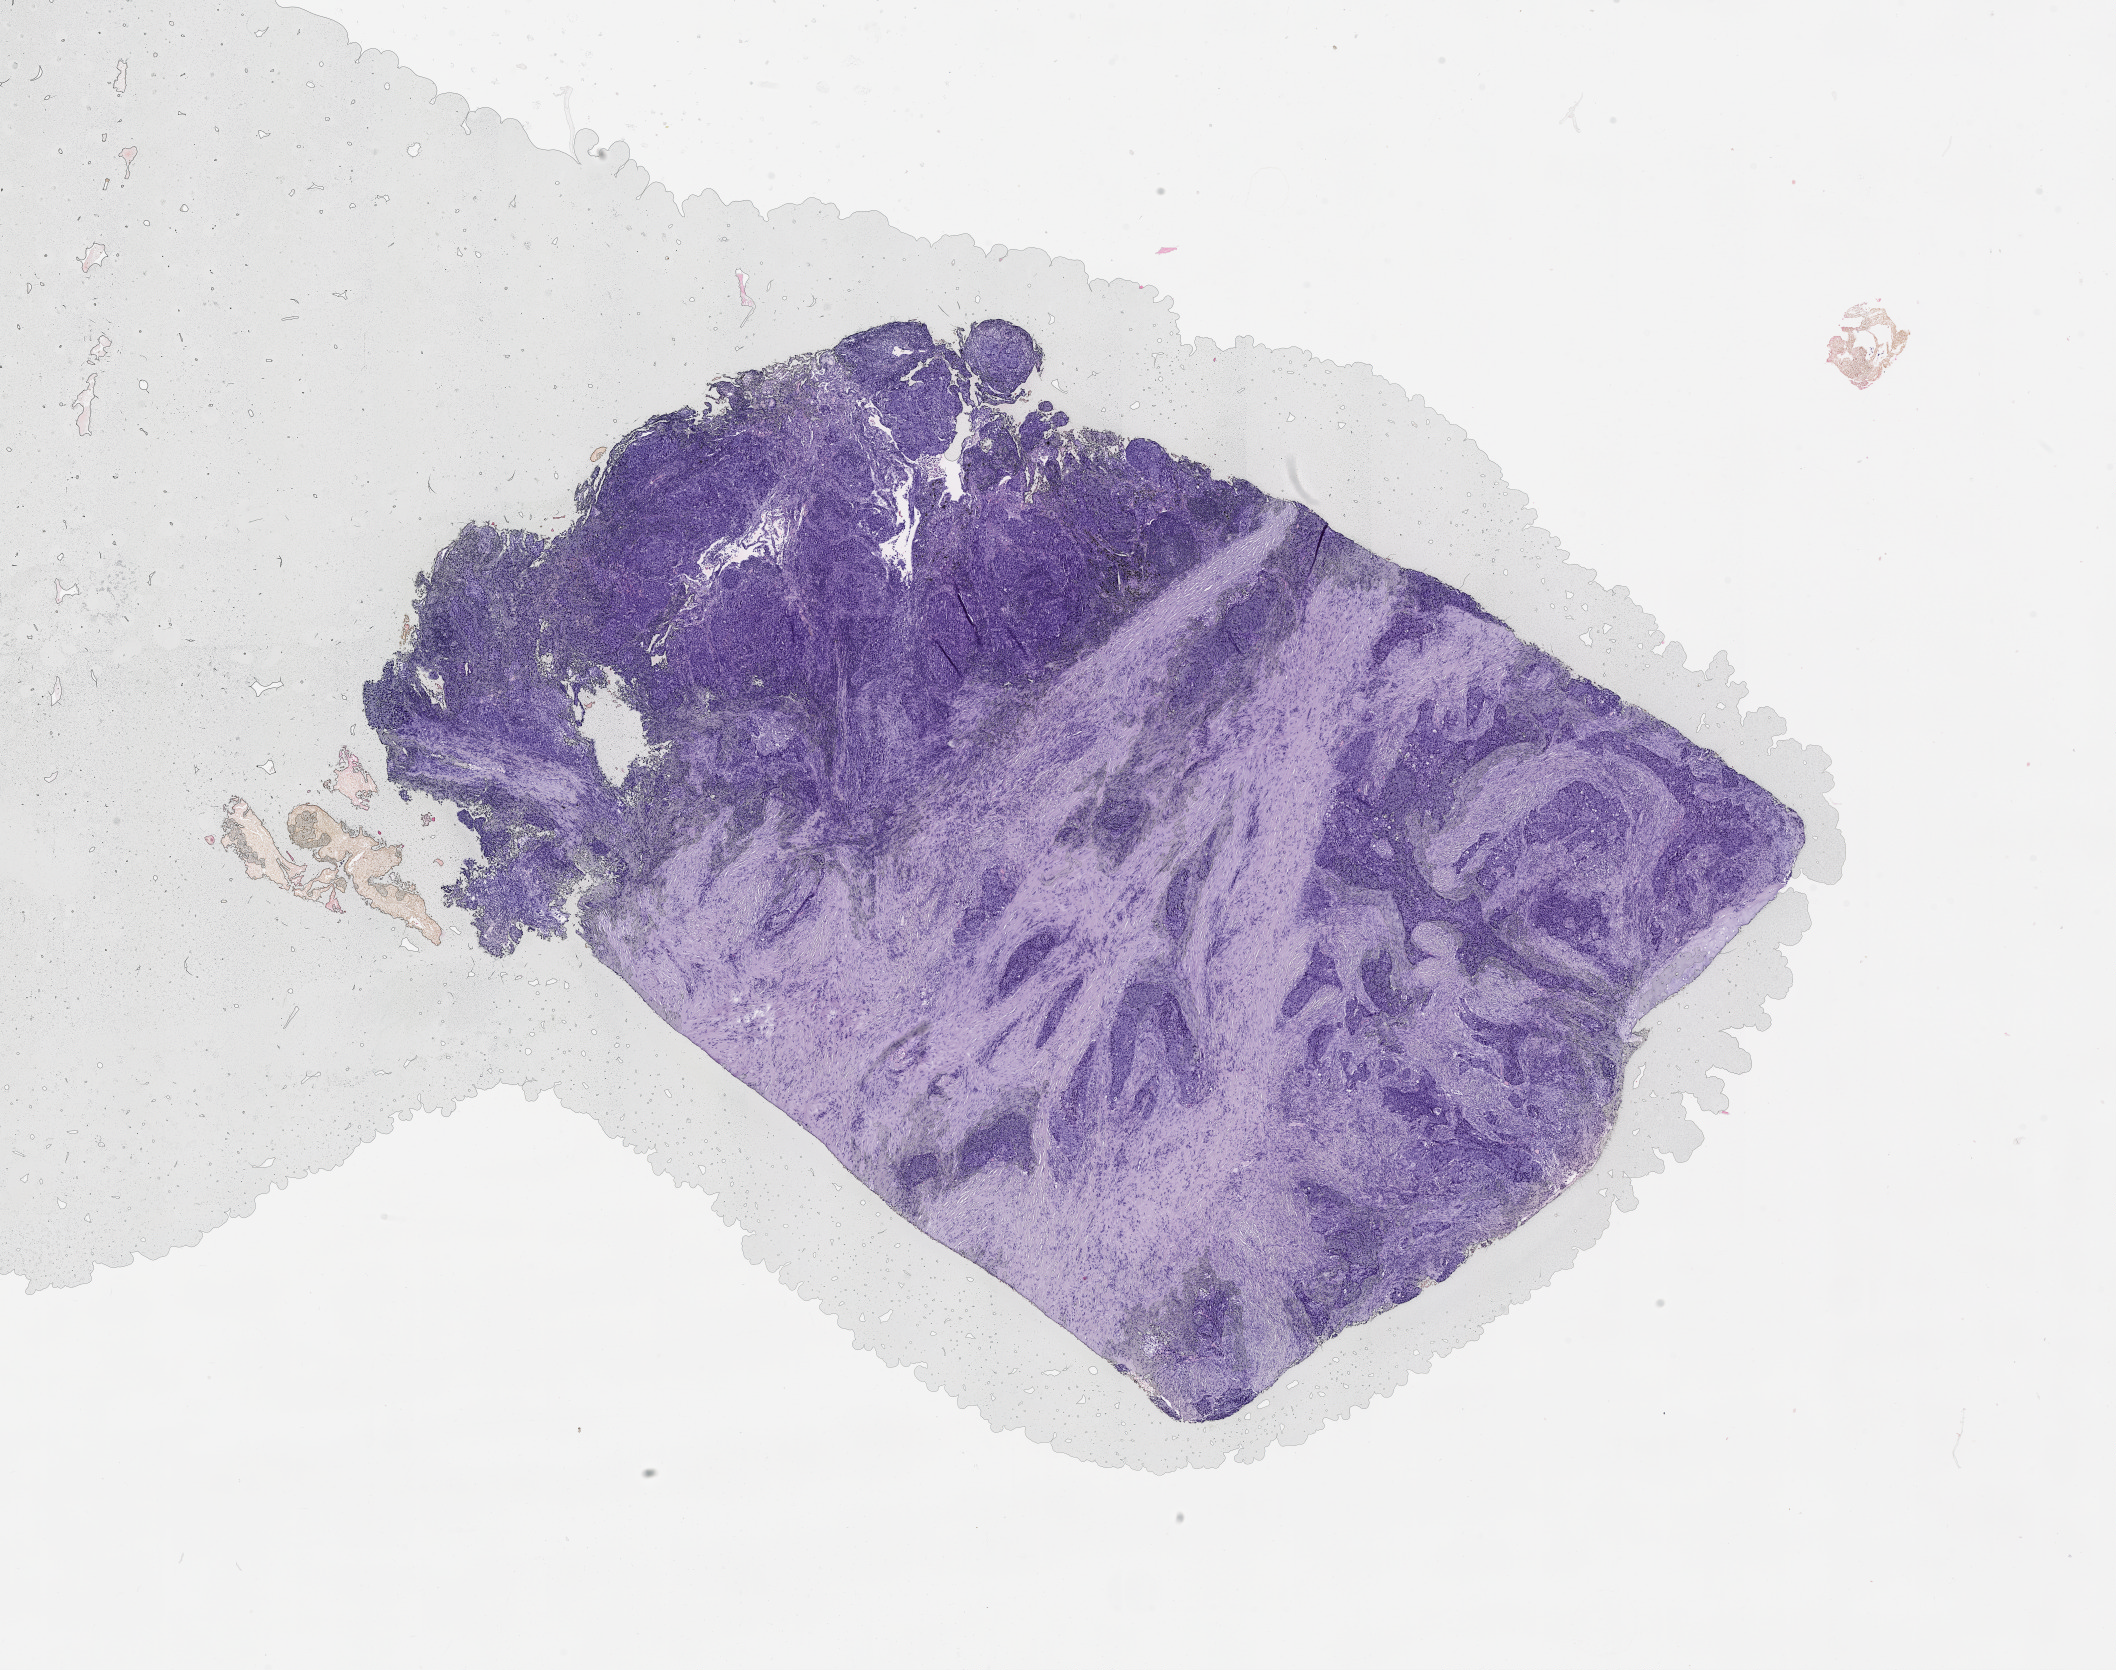
Hematoxylin and eosin (H&E) stained whole-slide image — shown as a low-resolution overview of the whole scanned area (about 17.0 x 13.4 mm), lung, tumour tissue. Patient: male, age 63 years.
Patient diagnosis (cohort enrolment): squamous cell carcinoma (lung).